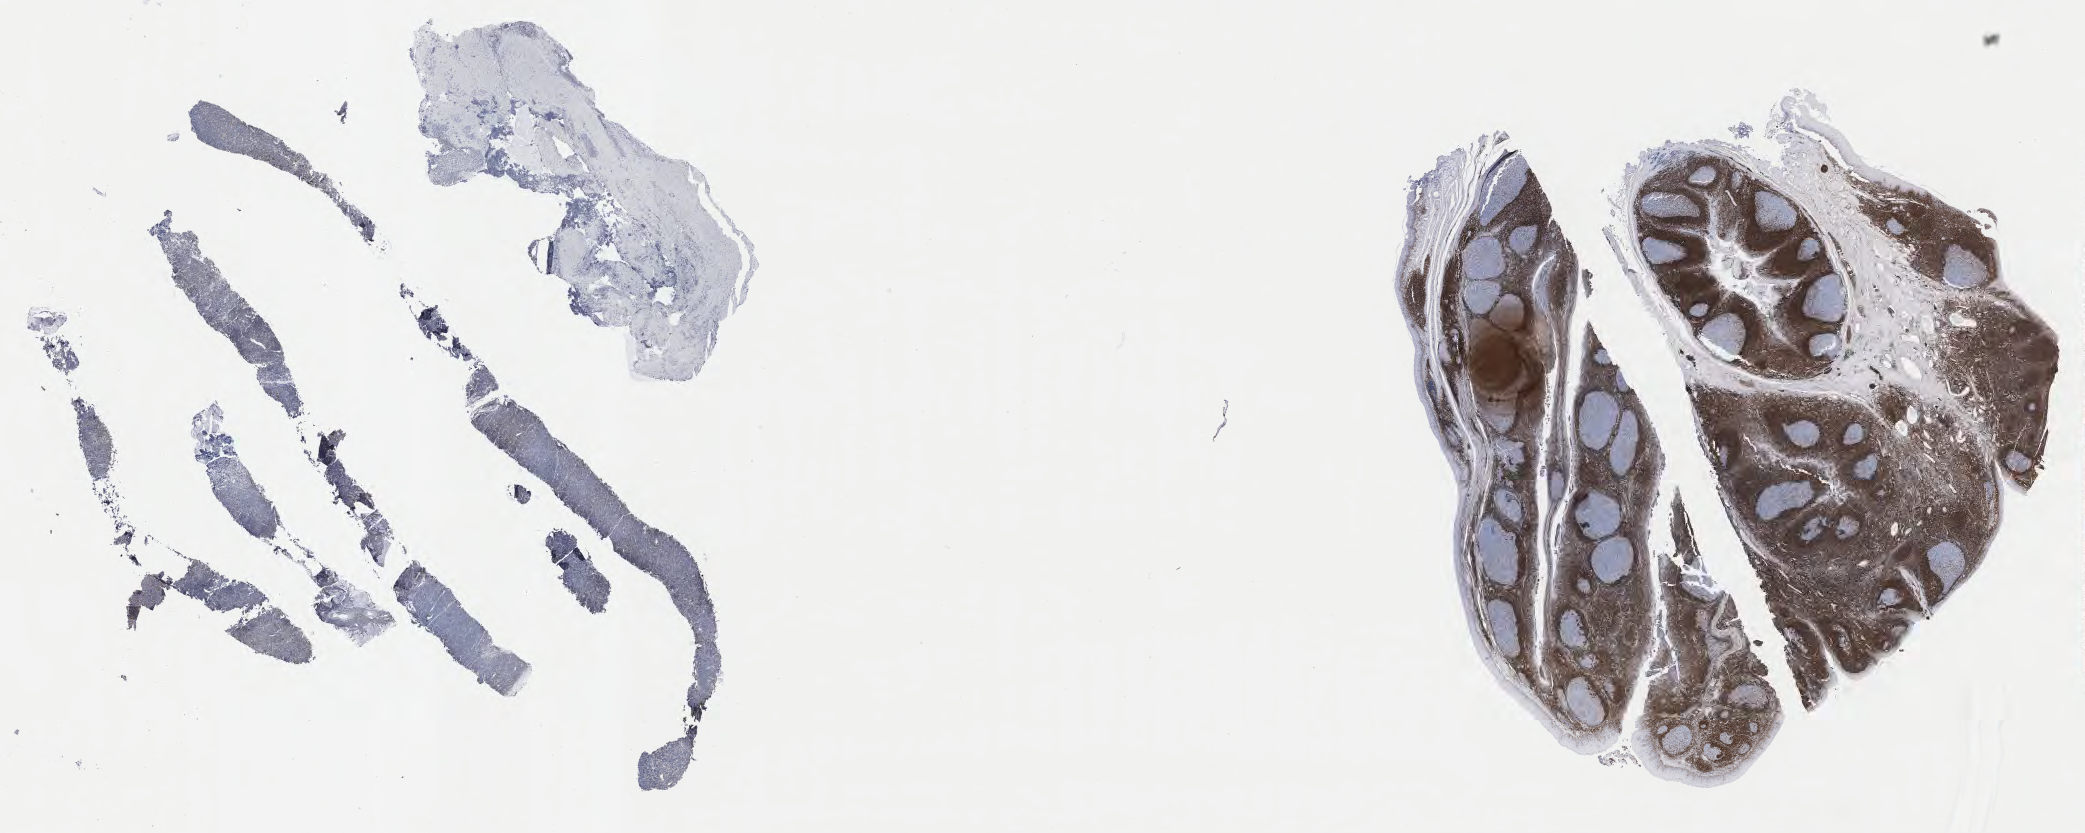
Immunohistochemistry (IHC) whole-slide image stained for BCL2, a low-resolution overview of the entire scanned area, about 33.7 x 13.5 mm; tumor tissue. Patient male; 29 years old.
Histologic diagnosis: Burkitt lymphoma, NOS.